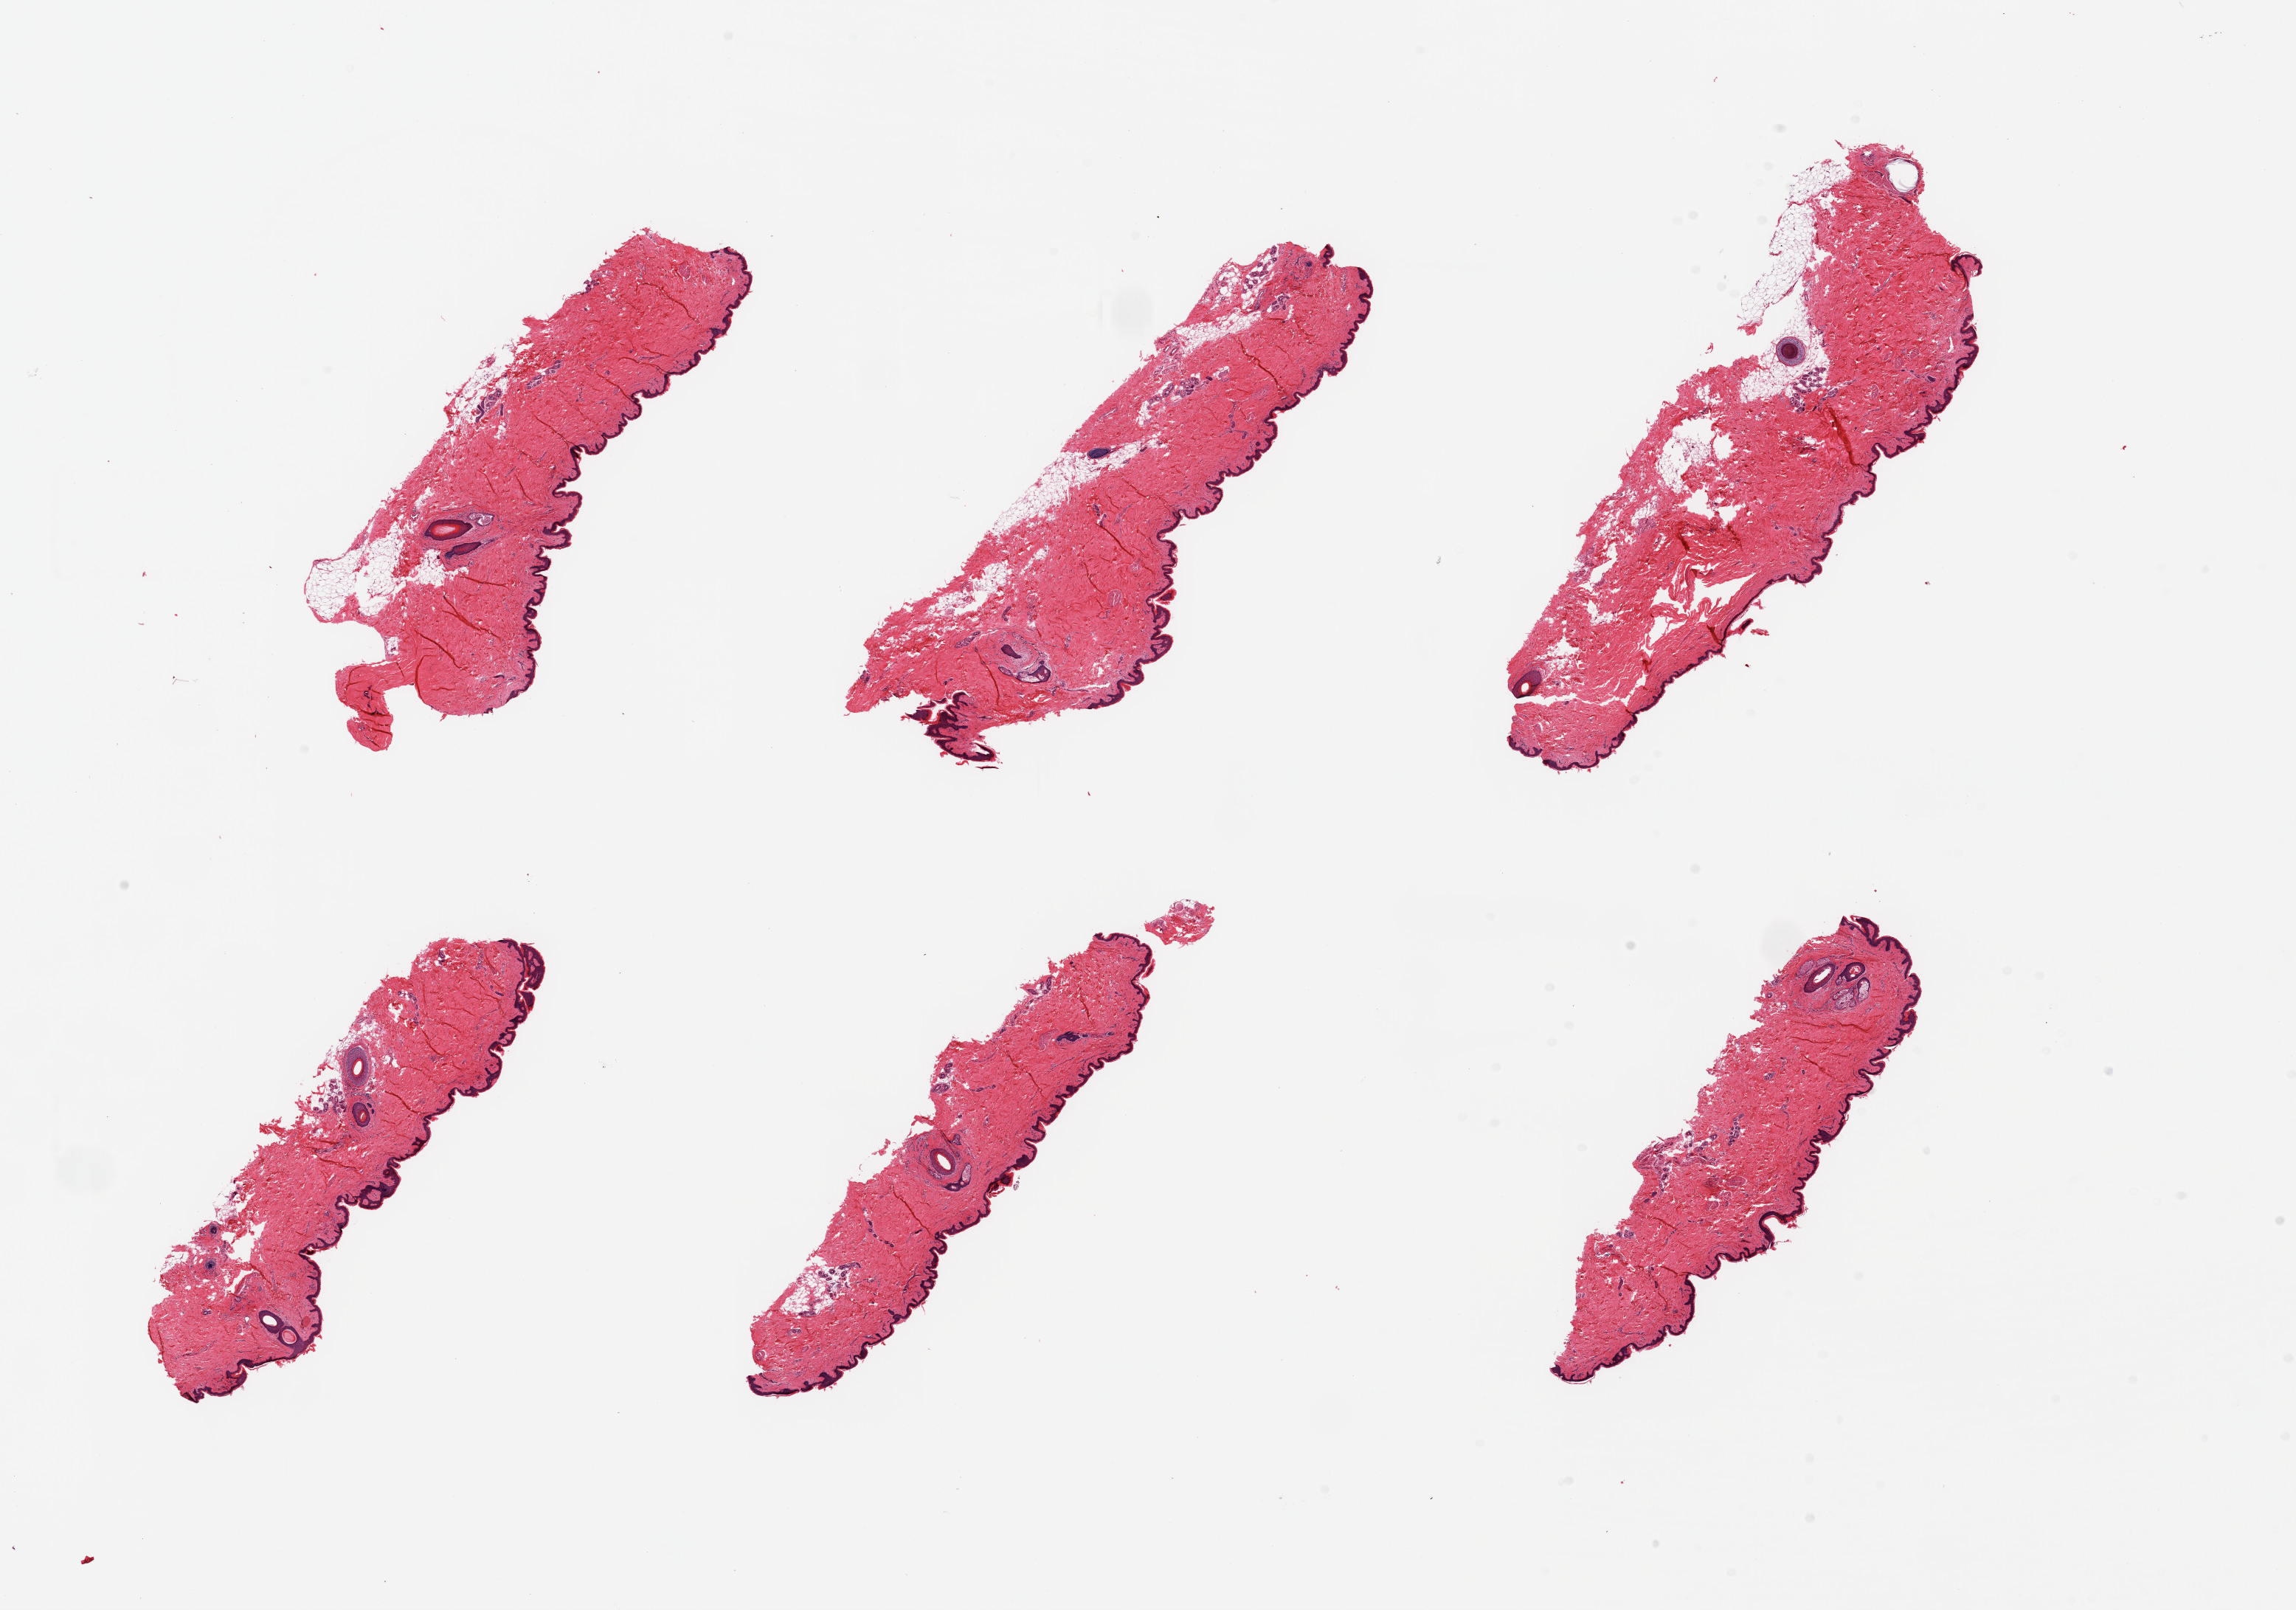
Hematoxylin and eosin (H&E) whole-slide image, shown as a low-resolution overview of the whole scanned area (about 24.6 x 17.3 mm), PAXgene-fixed, paraffin-embedded tissue, section of skin of suprapubic region (target tissue), tissue donor sample. Donor: female.
- reviewer comment on this tissue sample: 6 pieces; well trimmed; up to 10% dermal fat; up to 2 hair follicles per piece